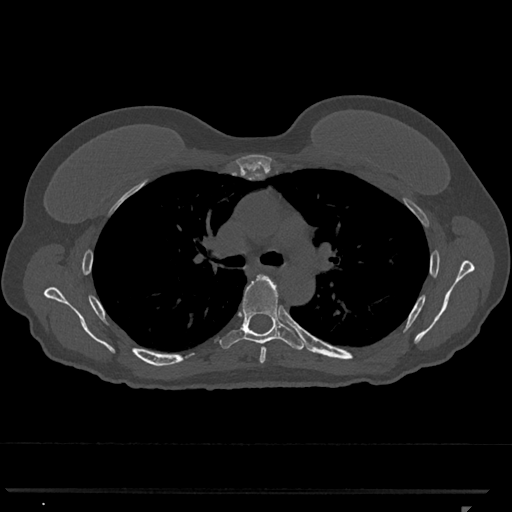
CT including the spine, one axial slice; slice 772 of 793 in the series (ordered by position); reconstruction kernel Br40s/3; 120 kVp; bone window (W 1800 / L 400 HU); 0.5 mm slice thickness; 512 × 512 image matrix, field of view 380 × 380 mm. Patient: female, 62 years. Case-level facts recorded for this patient, not image findings: primary cancer: renal.
Structures marked on this image (semi-automatic segmentation, software-assisted and operator-edited):
- T5 vertebra: bounding box [x1, y1, x2, y2] px = [259, 290, 278, 363]
- T6 vertebra: [220, 274, 305, 350]